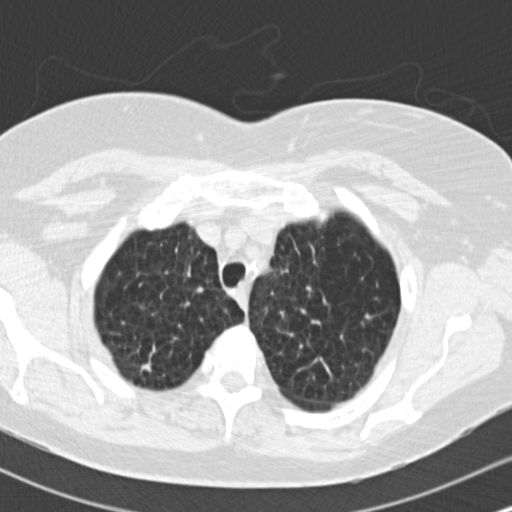
Low-dose screening chest CT, axial slice, baseline screening round, lung window (W 1500 / L -600 HU), 2 mm slice thickness, 120 kVp, slice 27 of 172 in the series. Female, age 73 years at enrolment. Former smoker at enrolment.
• Expert reader's lesion annotation, box from (x=119, y=343) to (x=173, y=387) px.
• The screening reader recorded 2 non-calcified nodules or masses ≥4 mm on this exam (right upper lobe, right upper lobe); which of them this box marks is not recorded.
• Later outcome: lung cancer diagnosed 601 days after this screen — adenocarcinoma, NOS, right upper lobe, moderately differentiated (G2), stage IB (AJCC 6th edition), 15 mm at pathology.